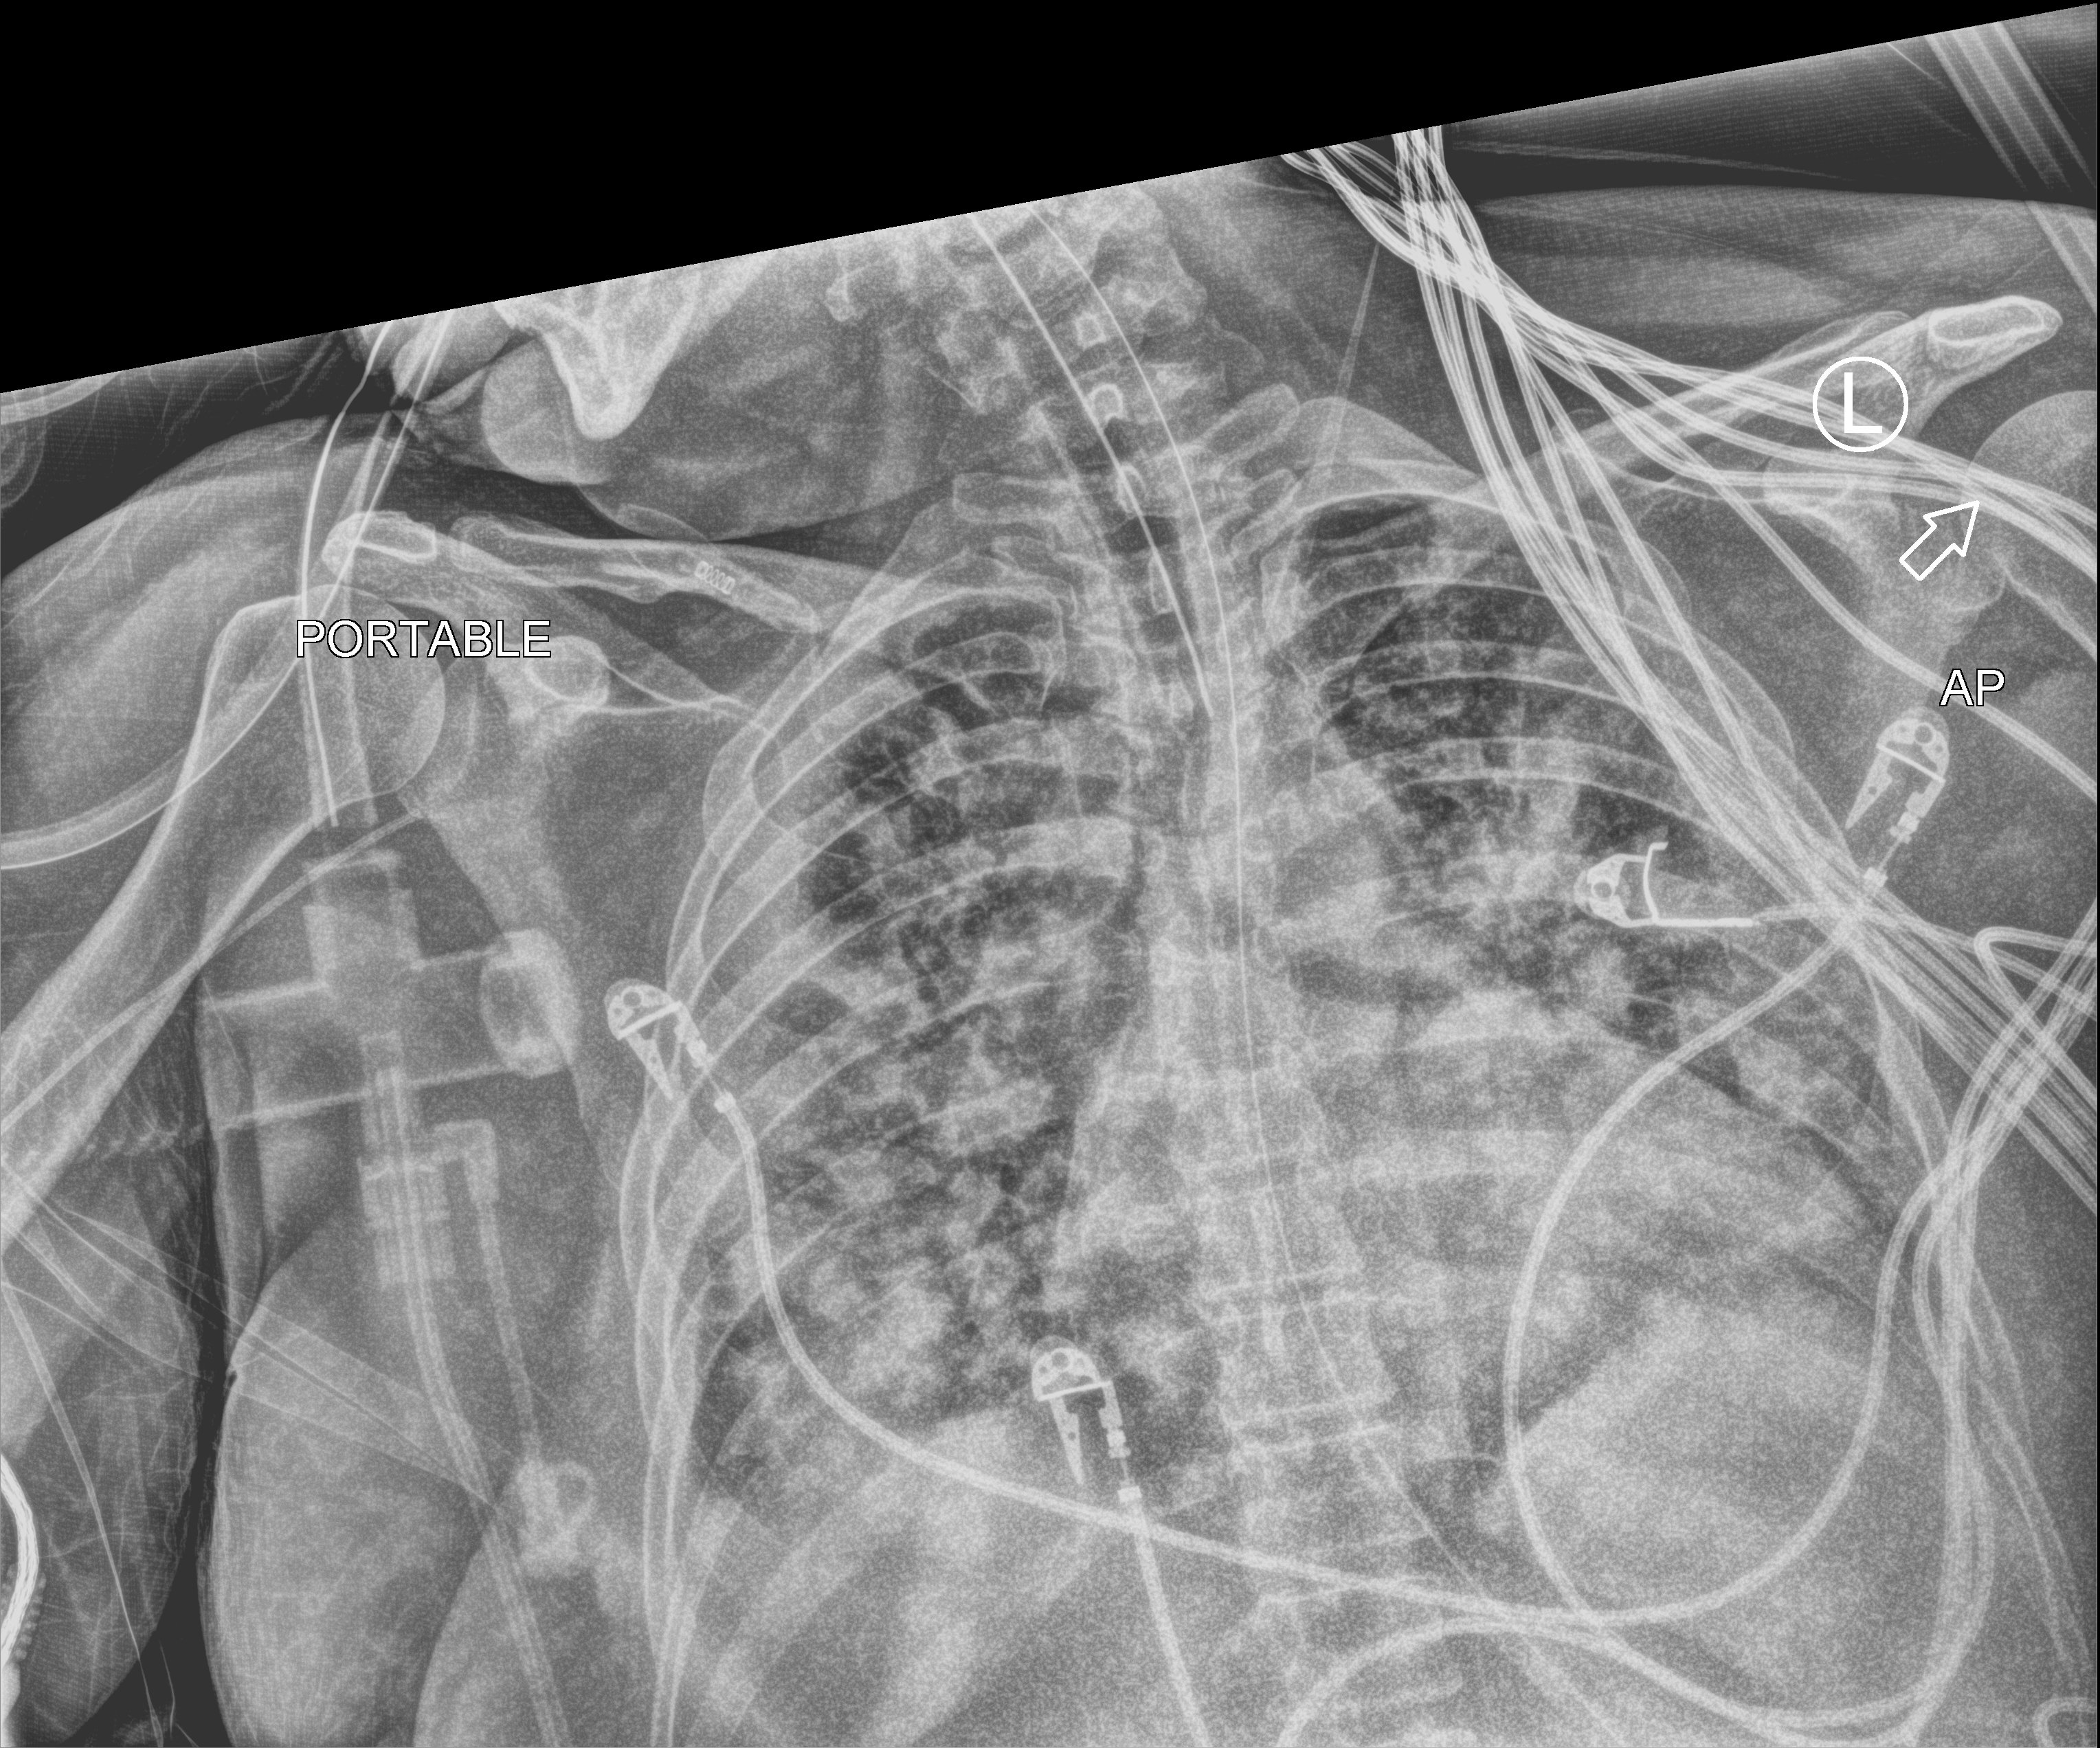
Portable chest radiograph; anteroposterior (AP) projection. Female patient hospitalised with COVID-19, age 18–59 years.
From the hospital-stay record, not from the radiograph (when in the stay this image was taken is not recorded): mechanically ventilated during this hospital stay: yes; admitted to intensive care during this hospital stay: yes.